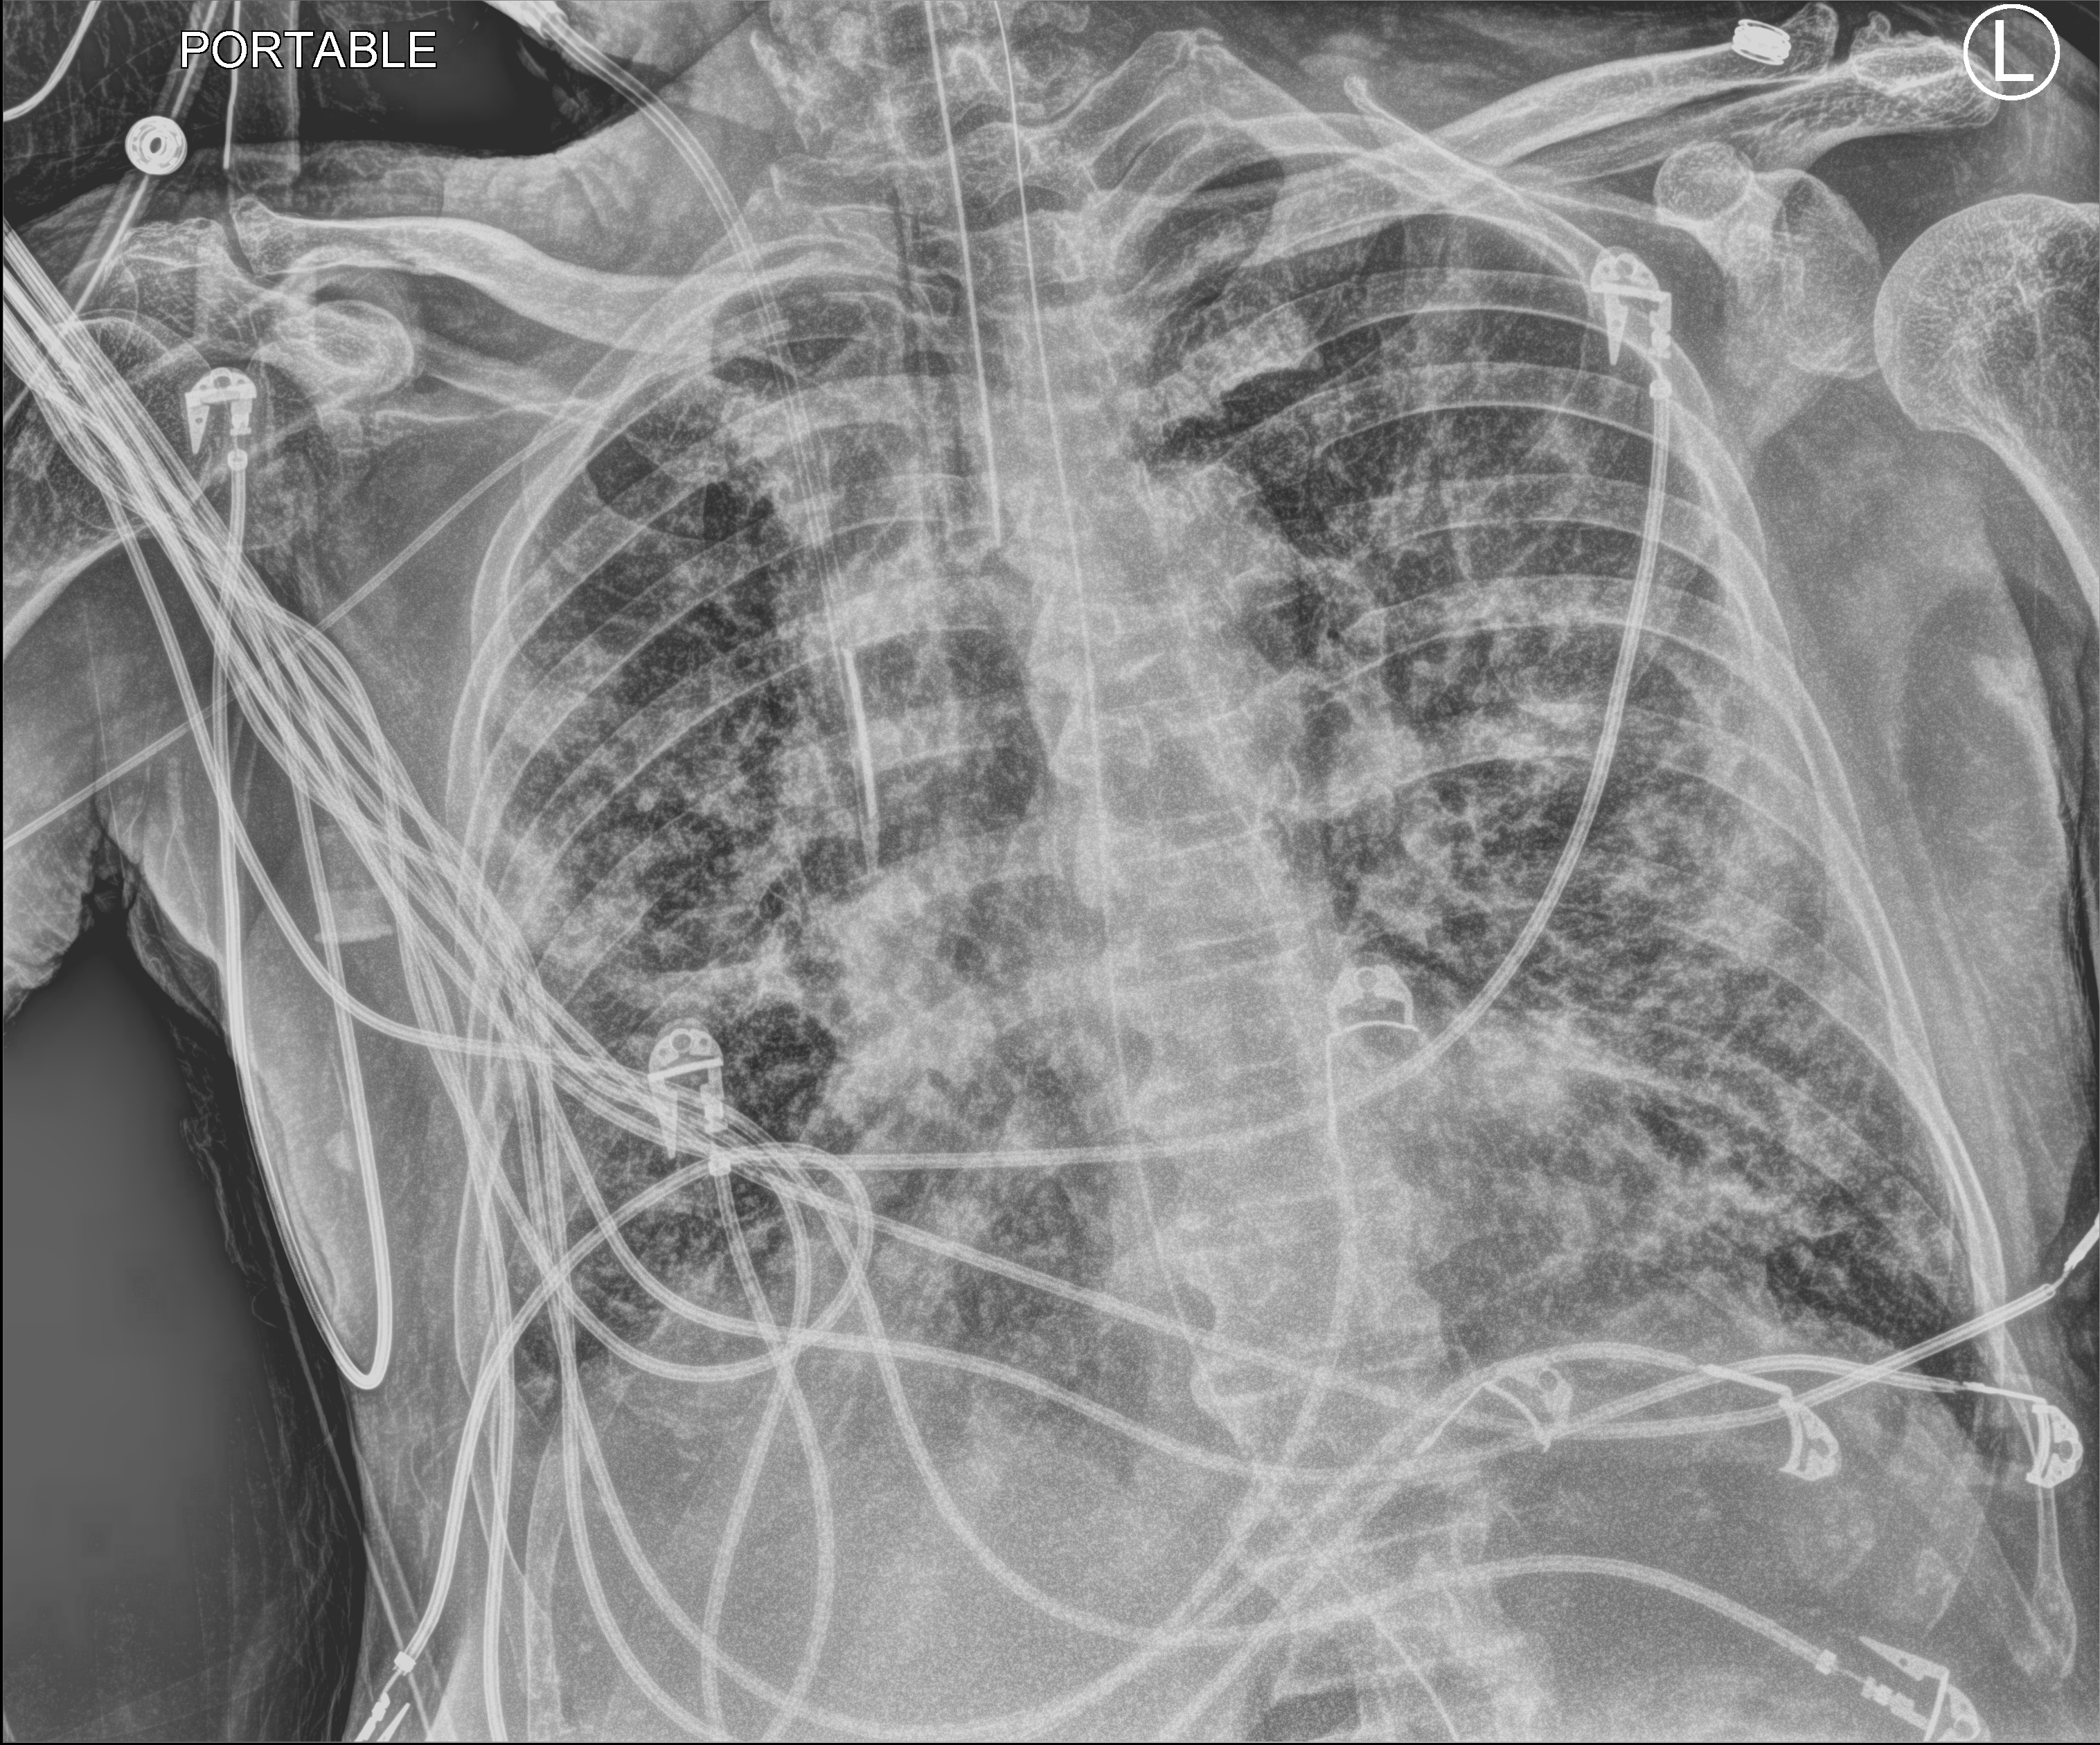
Portable chest radiograph. Patient hospitalised with COVID-19; male, aged 60–74 years.
Hospital-stay facts (about this admission, not read from this image; timing relative to this image not recorded):
- chronic kidney disease (admission record): no
- mechanically ventilated during this hospital stay: yes